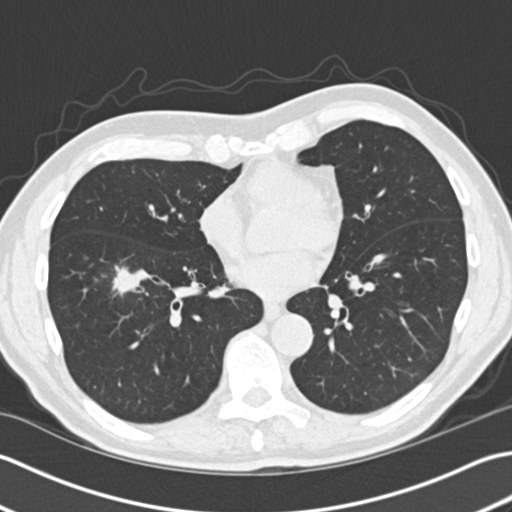
Axial slice from a low-dose chest CT screening exam. Second screening round (one year after baseline). Lung window (W 1500 / L -600 HU). 2 mm slice thickness. 120 kVp. Slice 103 of 172 in the series. 512 × 512 image matrix. Male participant, aged 73 years at enrolment.
Lesion marked by an expert reader, bounding box <93,252,151,314> (left, top, right, bottom; pixels). Reader record for this screening exam (exam-level; its link to the box is not recorded): non-calcified nodule or mass ≥4 mm, right lower lobe, 18 × 15 mm, spiculated (stellate) margins, soft tissue attenuation, pre-existing on the prior screen: yes. Official screen result: positive, other. Lung cancer was diagnosed 87 days after this screen: non-small cell carcinoma, right lower lobe, stage IA (AJCC 6th edition), 30 mm at pathology.